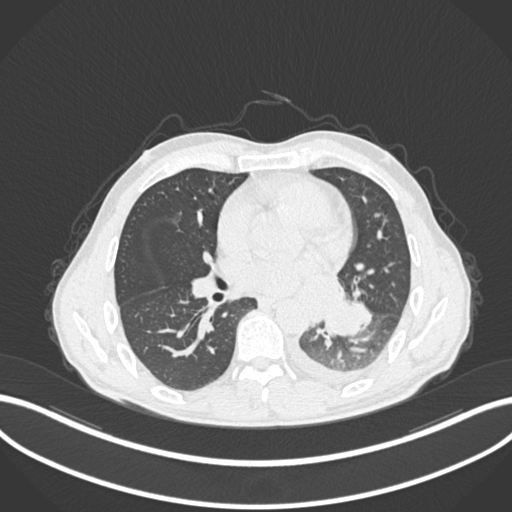
Chest CT, one axial slice. Position 116 of 222 along the scan axis. Reconstruction kernel B30f. 120 kVp. Lung window (W 1500 / L -600 HU). 1 mm slice thickness. 512 × 512 image matrix, field of view 400 × 400 mm. Patient: male, 47 years. From the clinical record (not read from this slice): clinical TNM (as recorded): T3 N1 M1c.
Annotated regions visible in this slice (bounding box drawn by a radiologist):
- lung tumour (recorded histology: small cell carcinoma): bounding box [x1, y1, x2, y2] px = [324, 296, 364, 338]